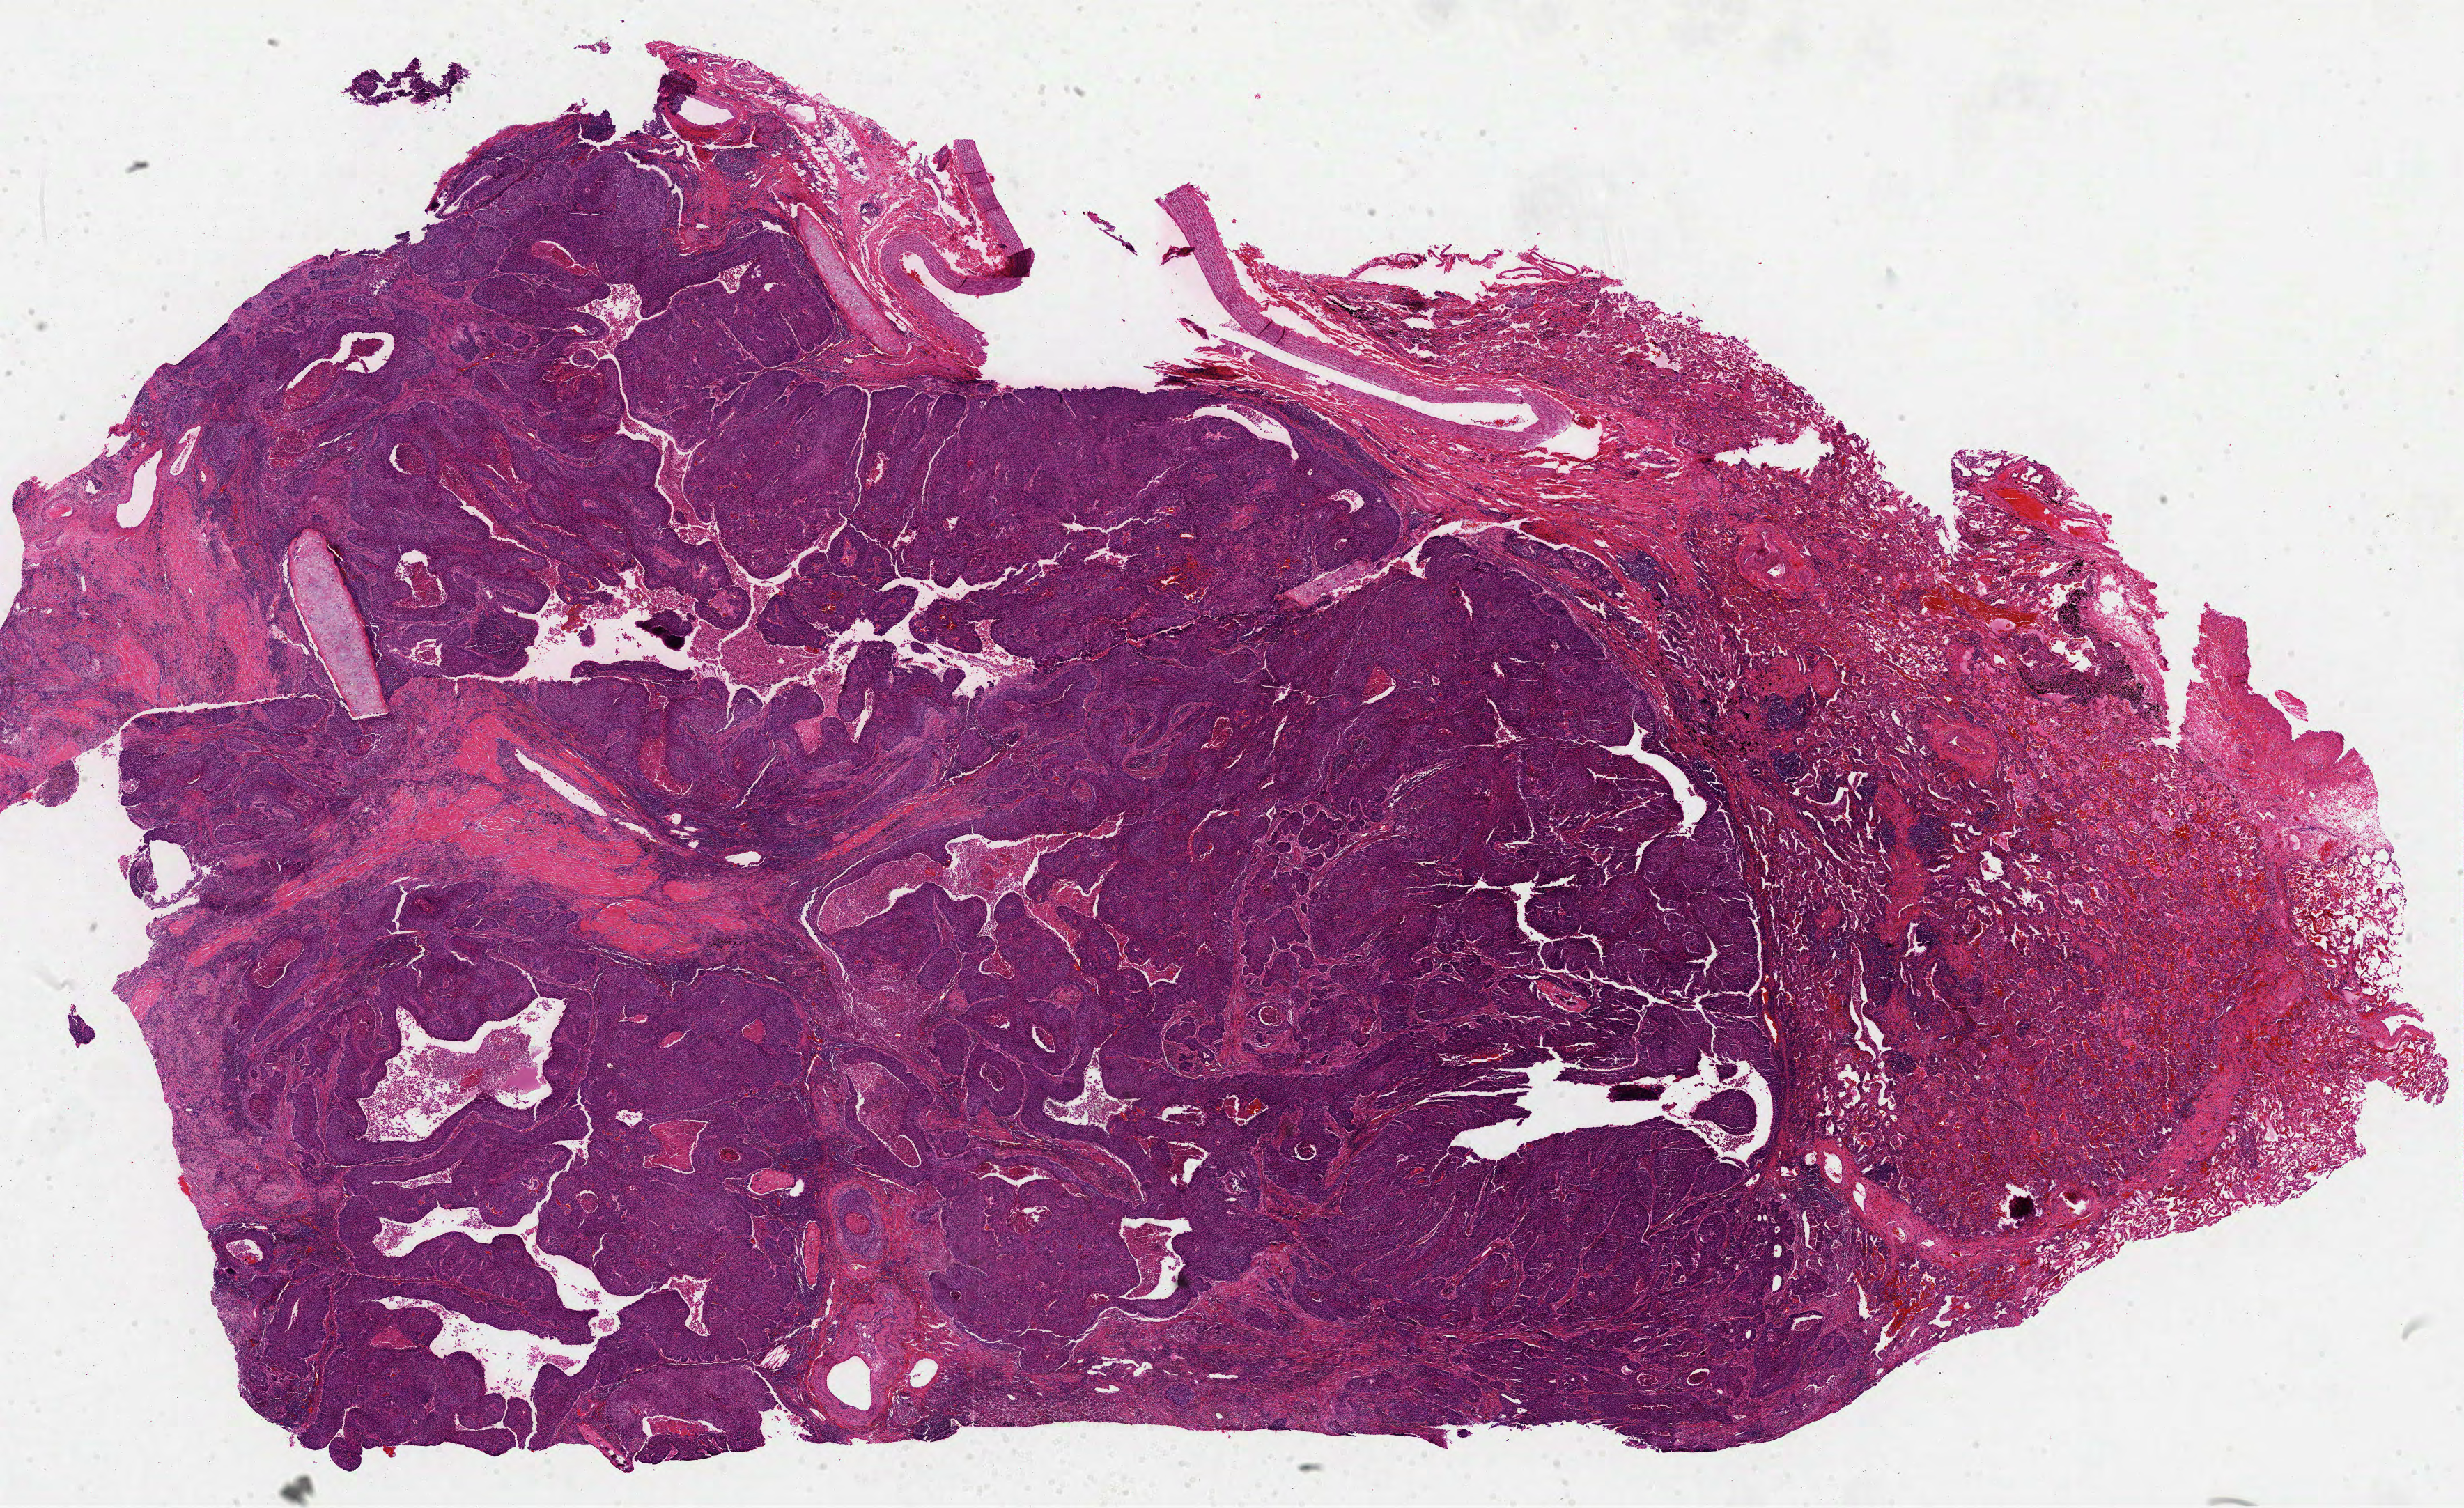
Digitized Hematoxylin and eosin (H&E) stained tissue section (whole slide) — a low-resolution overview of the entire scanned area, about 28.5 x 17.5 mm (from a 40x scan), FFPE section, lung, primary tumour sample. Male, age 66 years at initial diagnosis.
- laterality: left
- TNM: T2 N2 M0
- AJCC pathologic stage: IIIA (6th edition)
- diagnosis: Squamous cell carcinoma, NOS (upper lobe, lung)